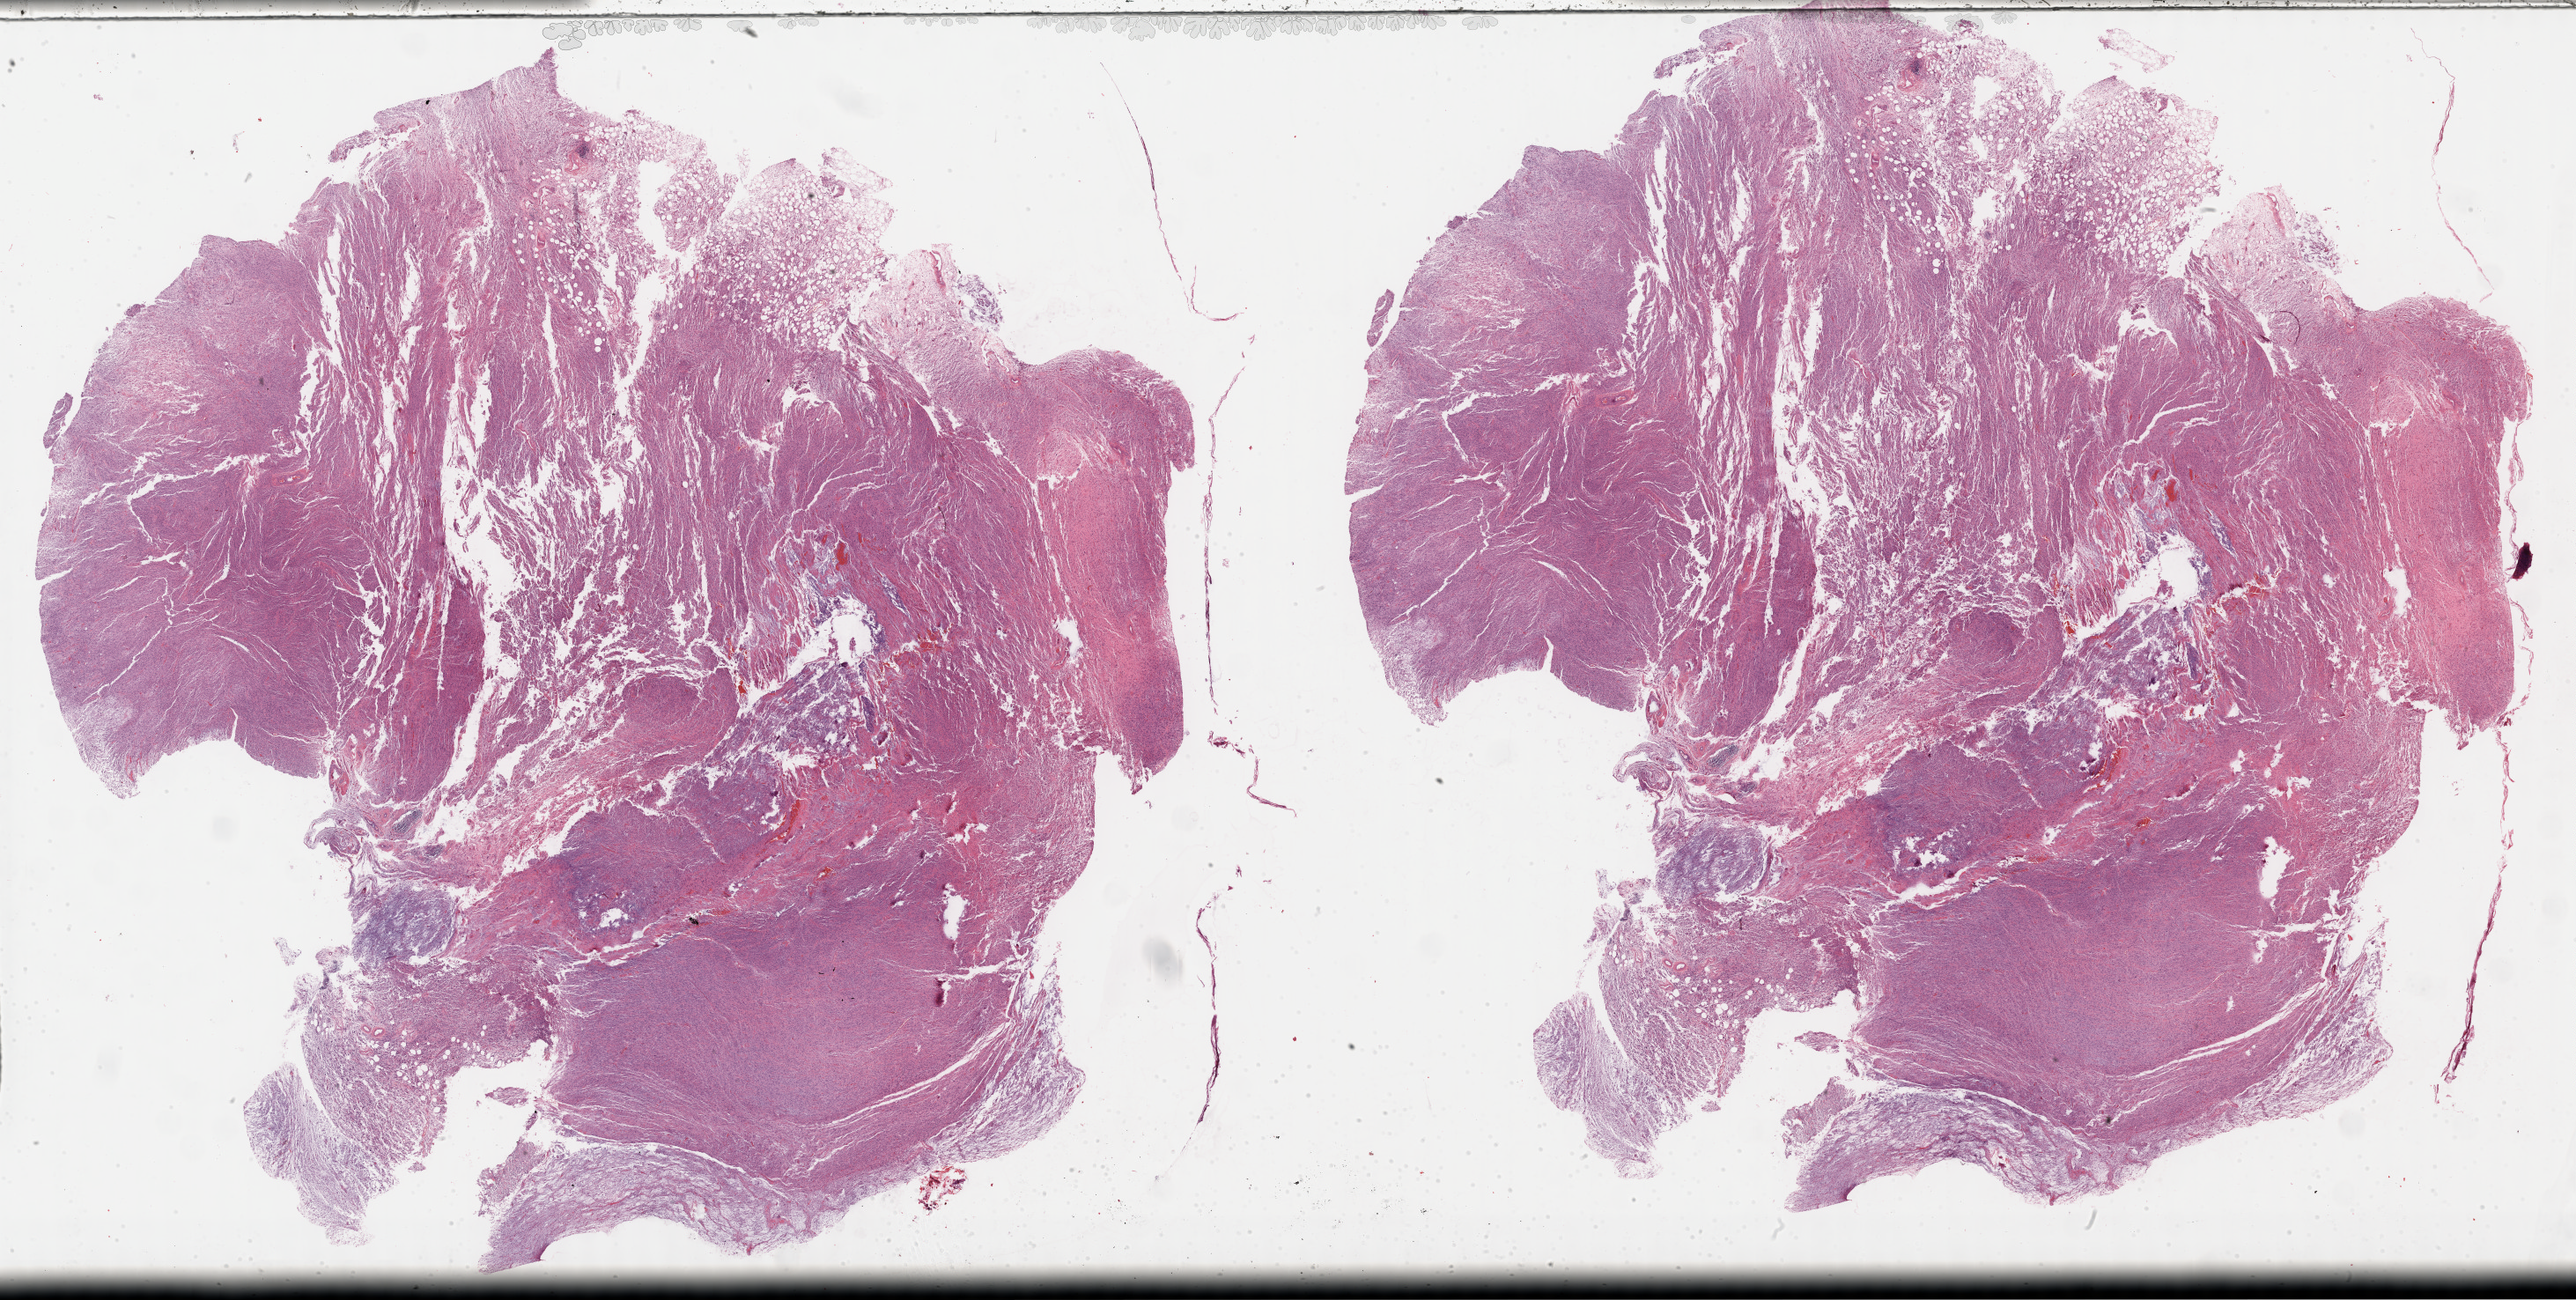
Whole-slide histology image, Hematoxylin and eosin (H&E) stained — low-resolution overview of the scanned area, about 47.3 x 23.9 mm (slide scanned at 40x). Formalin-fixed paraffin-embedded (FFPE) diagnostic section. Primary tumour sample from the connective, subcutaneous and other soft tissues. Patient: male, age at initial diagnosis 59 years.
Pathologic diagnosis: Fibromyxosarcoma (connective, subcutaneous and other soft tissues of pelvis).